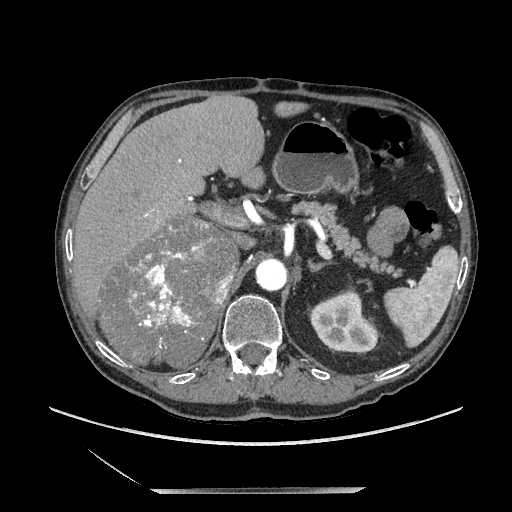
Contrast-enhanced abdominal CT, one axial slice; slice 135 of 243 in the series (ordered by position); soft-tissue window (W 400 / L 40 HU); 1.25 mm slice thickness; 512 × 512 image matrix. Male patient. Case-level facts recorded for this patient, not image findings: diagnosis: adrenocortical carcinoma; tumour side: right adrenal; tumour size at pathology: 16 cm; Ki-67 index: 17 %.
Annotated regions visible in this slice (semi-automatic segmentation, software-assisted and operator-edited):
- mass: bounding box <103,219,234,369> (left, top, right, bottom; pixels)